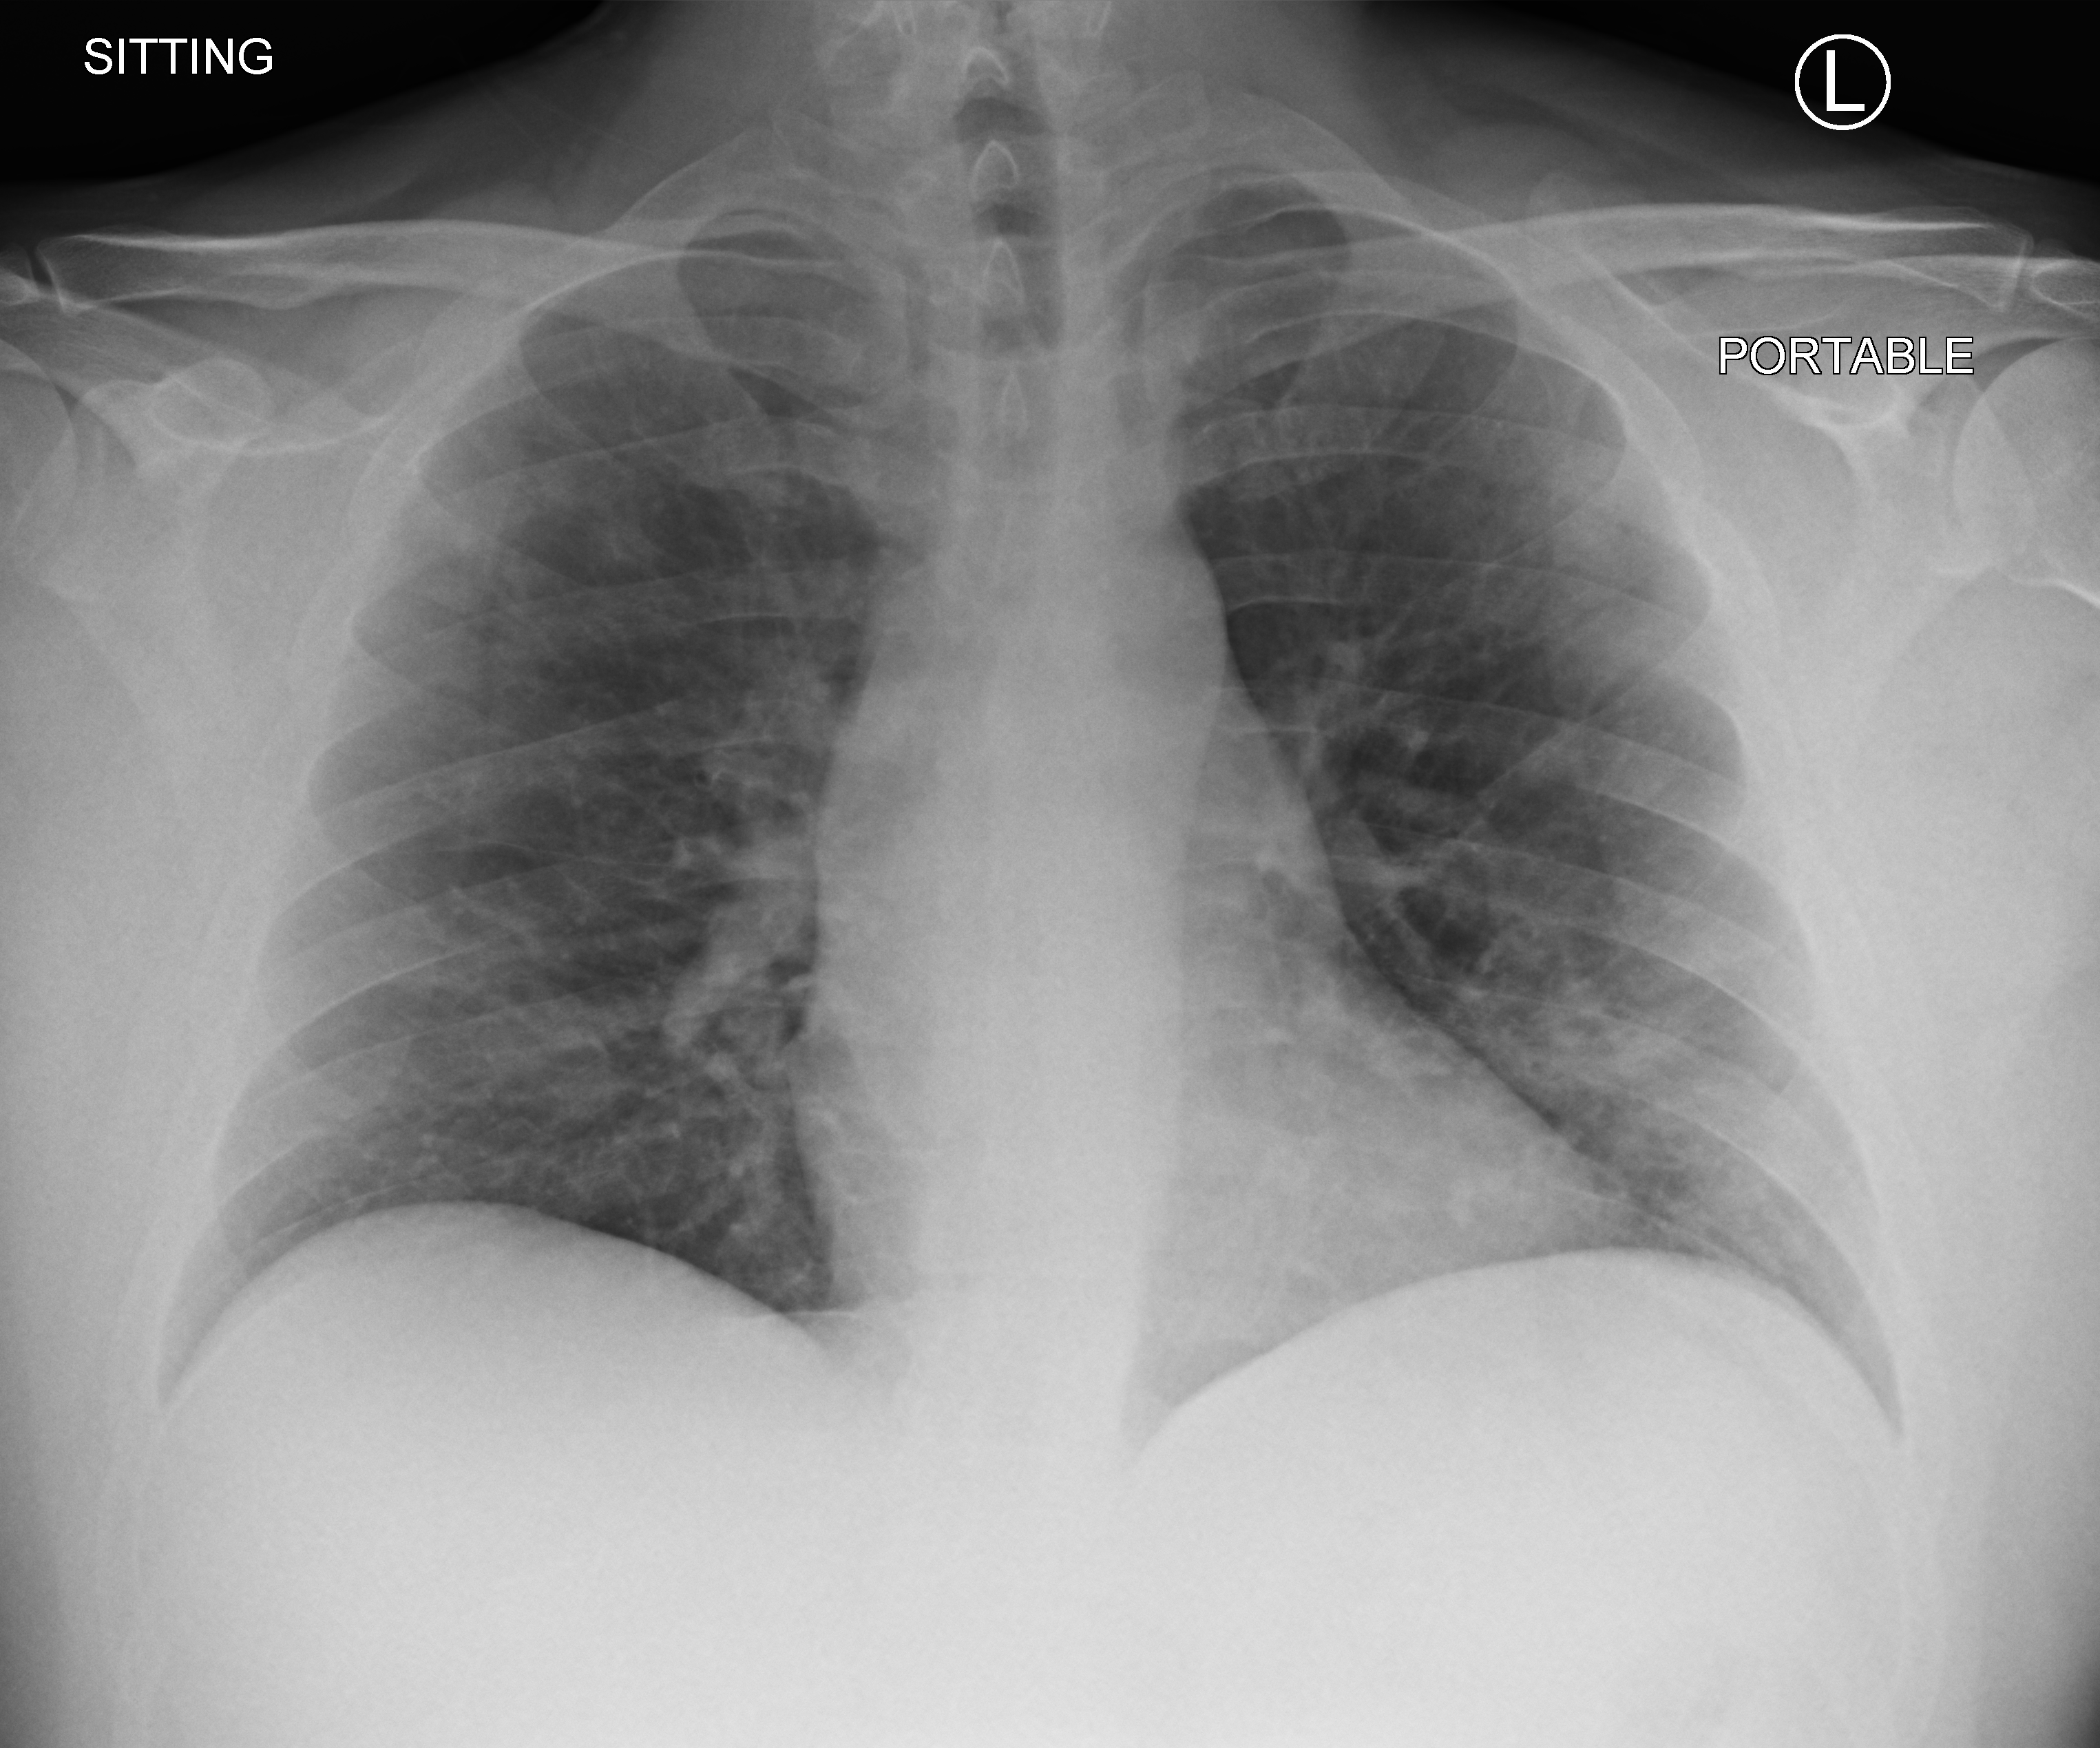
Bedside chest radiograph (computed radiography), anteroposterior (AP) projection. Patient hospitalised with COVID-19; male, aged 18–59 years.
From the hospital-stay record, not from the radiograph (when in the stay this image was taken is not recorded): other chronic lung disease (admission record): no; length of hospital stay: 1 day.